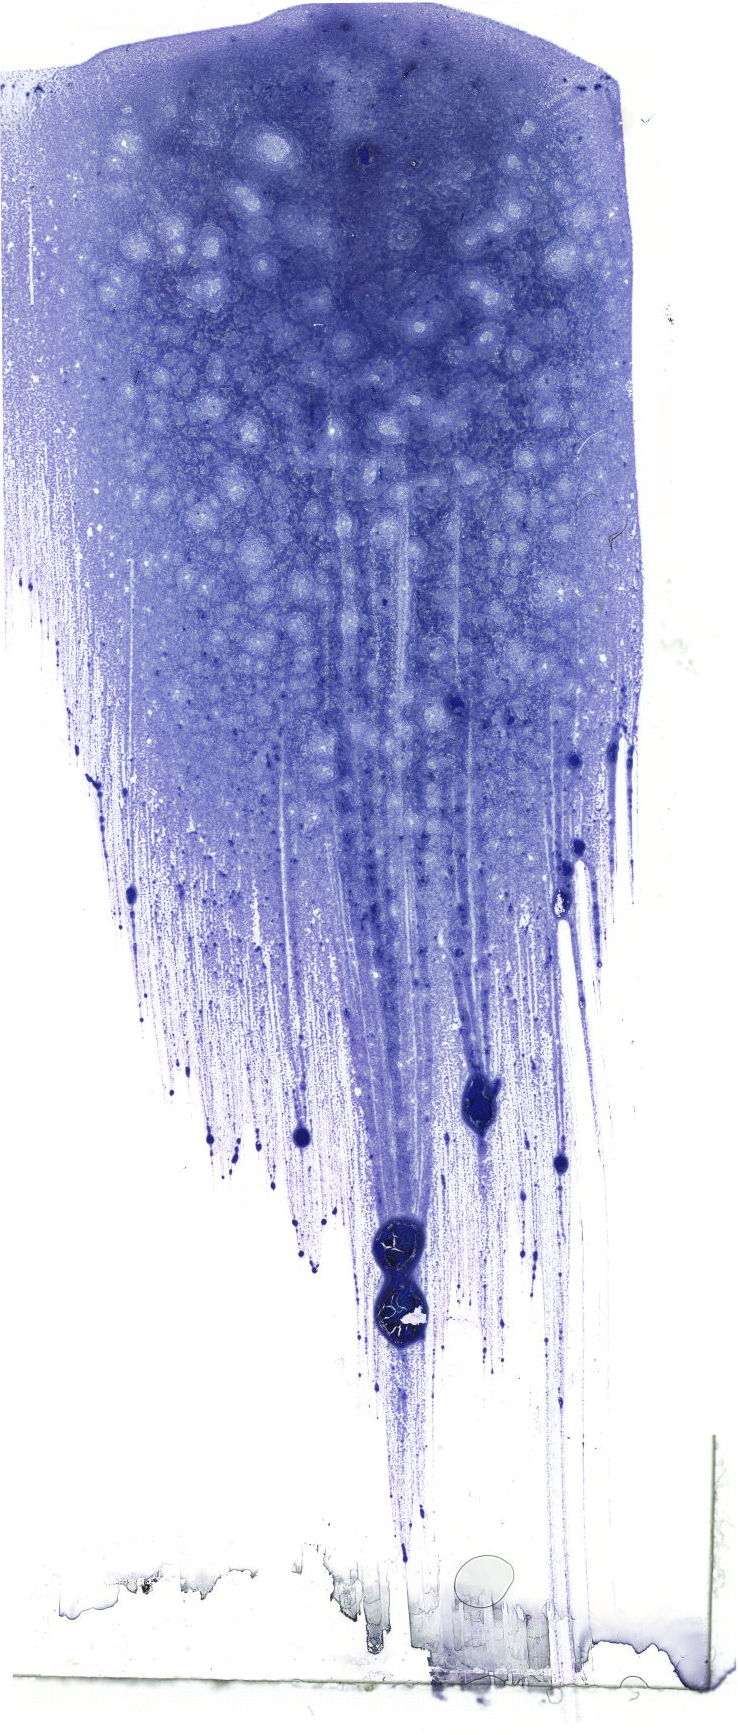
Whole-slide image of a May-Grünwald–Giemsa-stained bone marrow aspirate smear, low-resolution overview of the scanned area, about 20.9 x 49.2 mm. Patient sex: female.
- diagnosis: Chronic Phase Chronic Myeloid Leukemia, BCR-ABL1 Positive